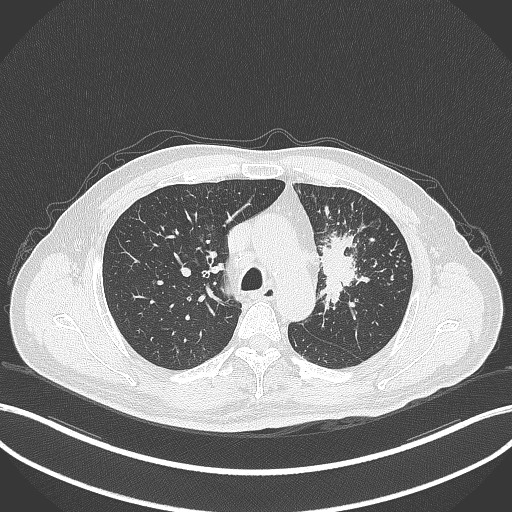
Chest CT, one axial slice. Slice 247 of 386 in the series (ordered by position). Reconstruction kernel B70f. 120 kVp. Lung window (W 1500 / L -600 HU). 512 × 512 image matrix, field of view 400 × 400 mm. Male patient, age 69 years. From the clinical record (not read from this slice): clinical TNM (as recorded): T2a N2 M0.
Outlined on this slice (rectangle marked by the reading radiologist):
- lung tumour (recorded histology: adenocarcinoma): bounding box [x1, y1, x2, y2] px = [312, 226, 366, 311]